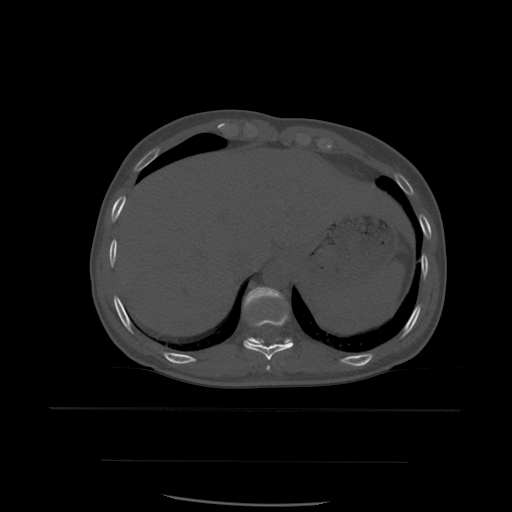
CT including the spine, one axial slice; slice 310 of 574 in the series (ordered by position); bone window (W 1800 / L 400 HU); 512 × 512 image matrix, field of view 392 × 392 mm. Patient age 48 years. Case-level facts recorded for this patient, not image findings: primary cancer: lung.
Annotated regions visible in this slice (semi-automatically segmented with operator editing):
- T10 vertebra: bounding box <244,312,294,361> (left, top, right, bottom; pixels)
- T11 vertebra: <244,287,293,346>
- T9 vertebra: <266,366,271,371>